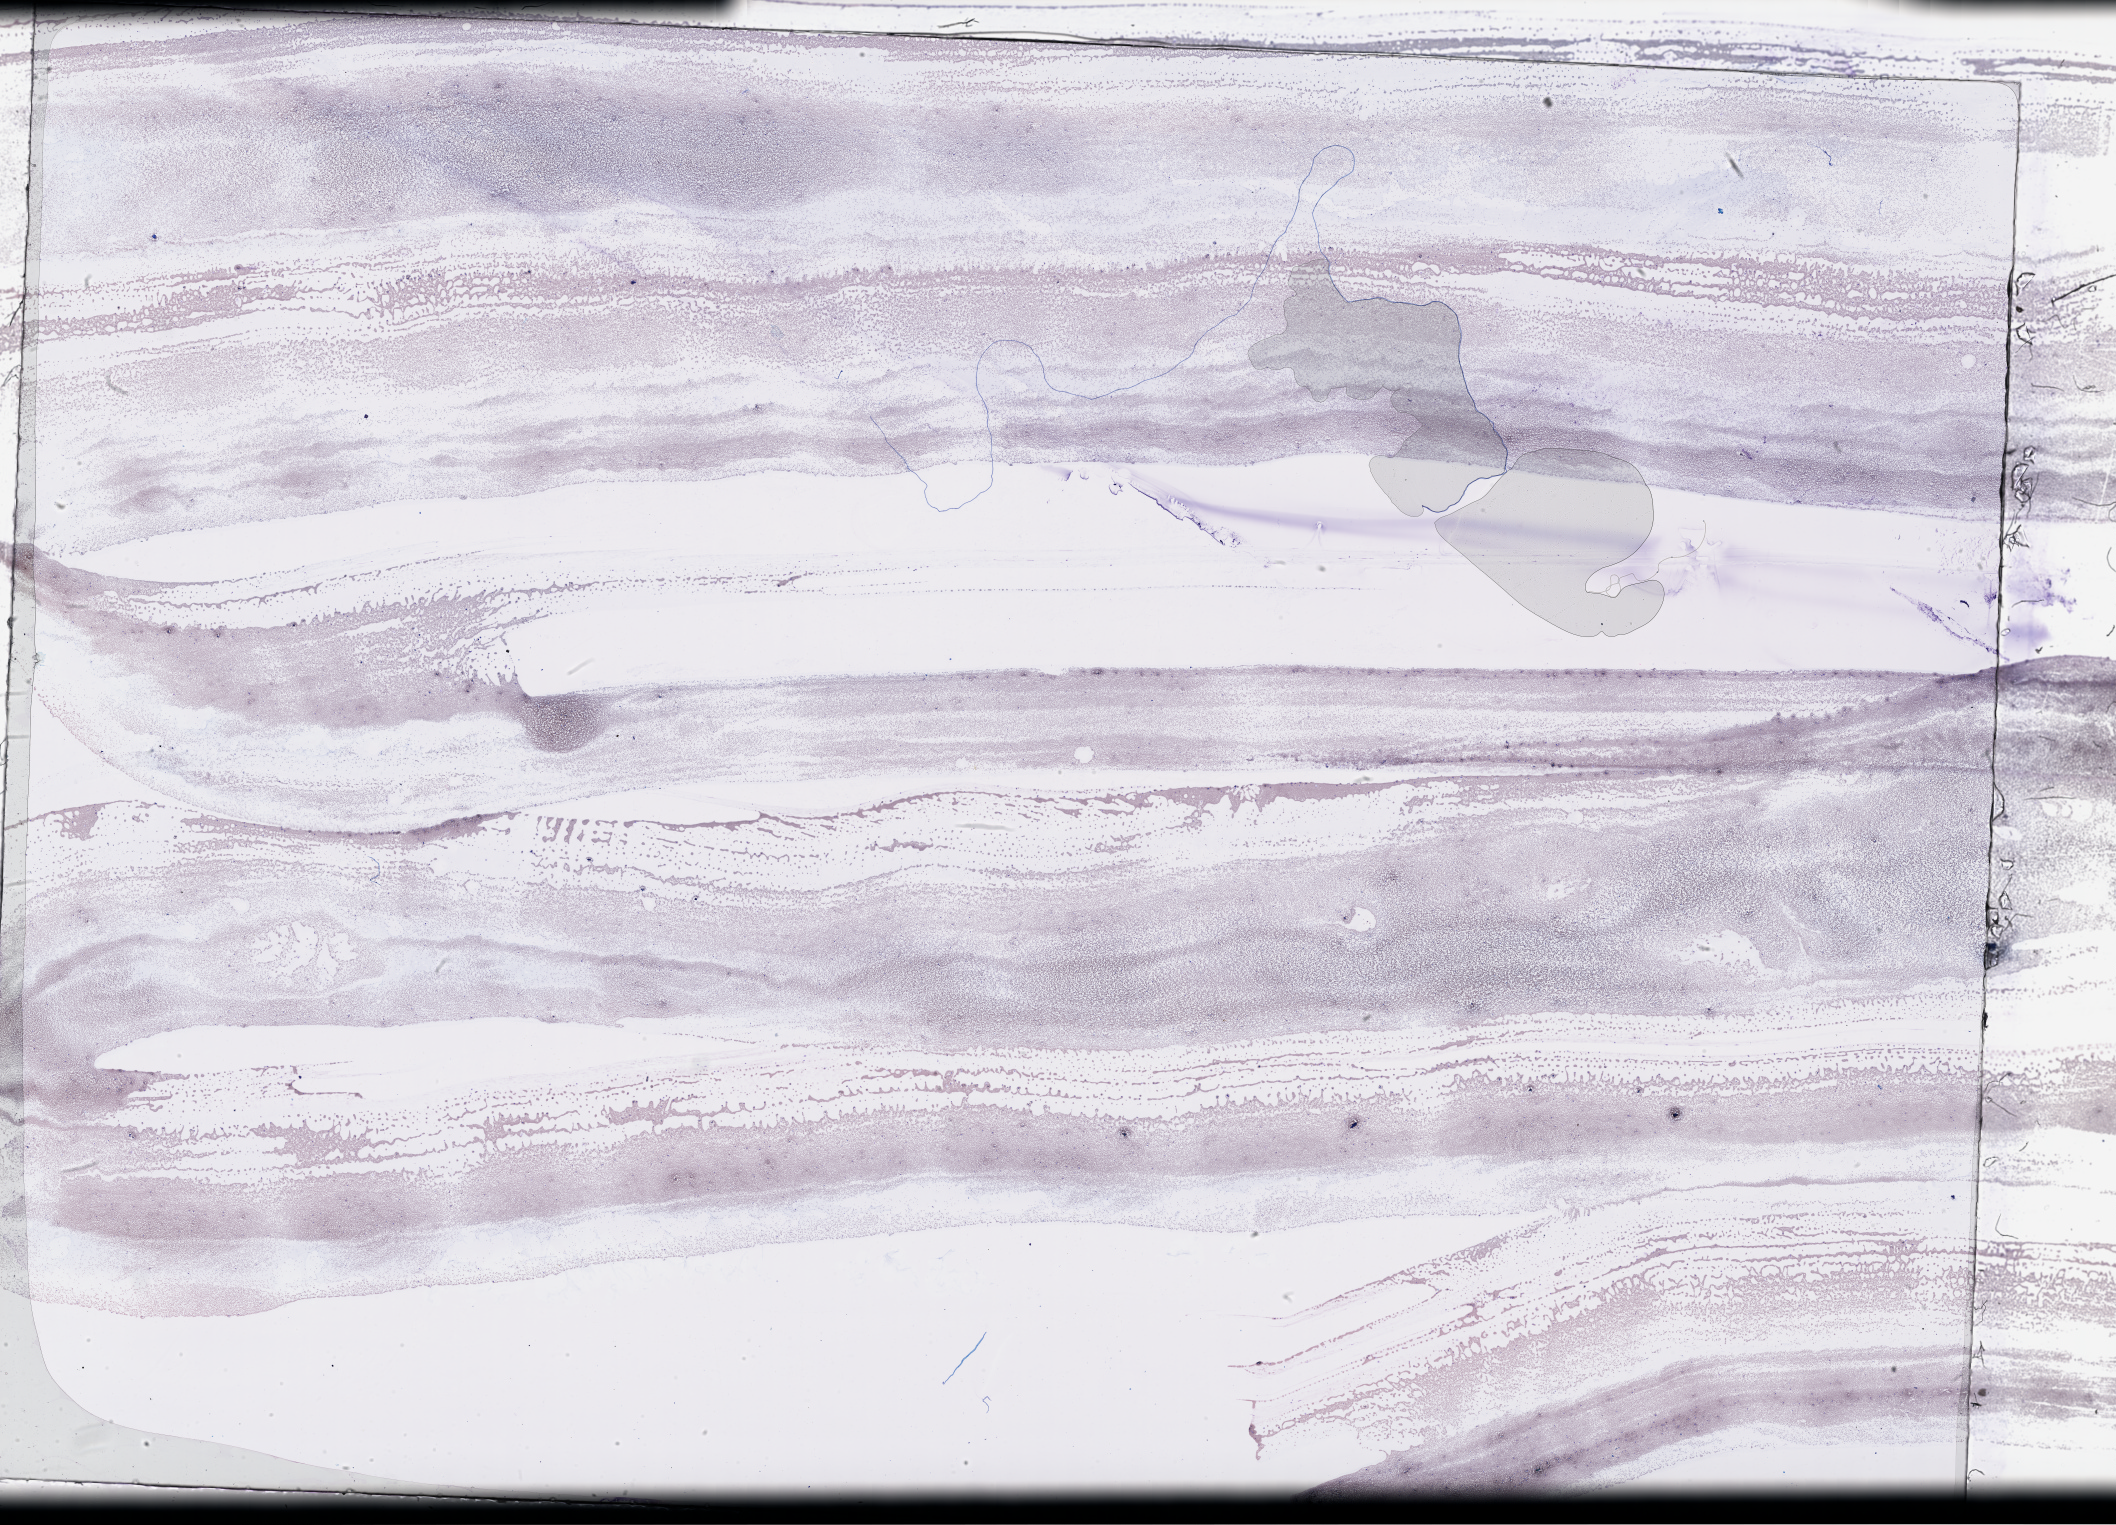
H&E whole-slide image, whole scanned area (about 34.2 x 24.6 mm) shown as a low-resolution overview; bone marrow (leukaemic) sample. Patient: female, age 45 years. Blasts: 50%.
Diagnosis: Acute Myeloid Leukemia. WHO classification: AML with inv(16)(p13.1q22) or t(16;16)(p13.1;q22); CBFB-MYH11. FAB classification: M4eos.